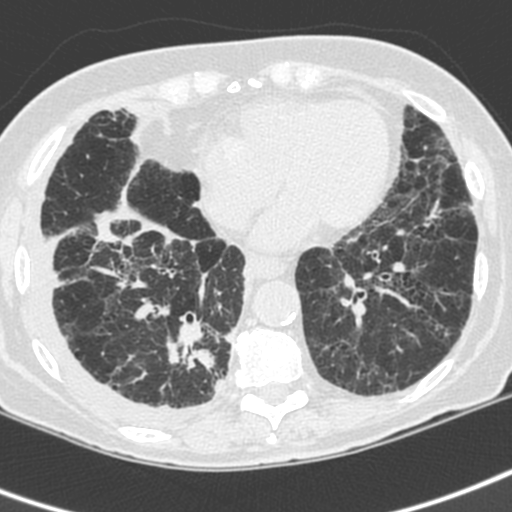
Chest CT (low-dose screening protocol), one axial image, baseline annual screen, lung window (W 1500 / L -600 HU), slice 131 of 192 in the series. Female participant, aged 73 years at enrolment. Current smoker at enrolment.
• Expert-annotated lung lesion, bounding box [x1, y1, x2, y2] px = [154, 314, 235, 406].
• Reader record for this screening exam (exam-level; its link to the box is not recorded): non-calcified nodule or mass ≥4 mm, right lower lobe, 35 × 30 mm, spiculated (stellate) margins, soft tissue attenuation.
• Participant outcome: lung cancer diagnosed 22 days after this screen — adenocarcinoma, NOS, right lower lobe, stage IV (AJCC 6th edition), 35 mm at pathology.